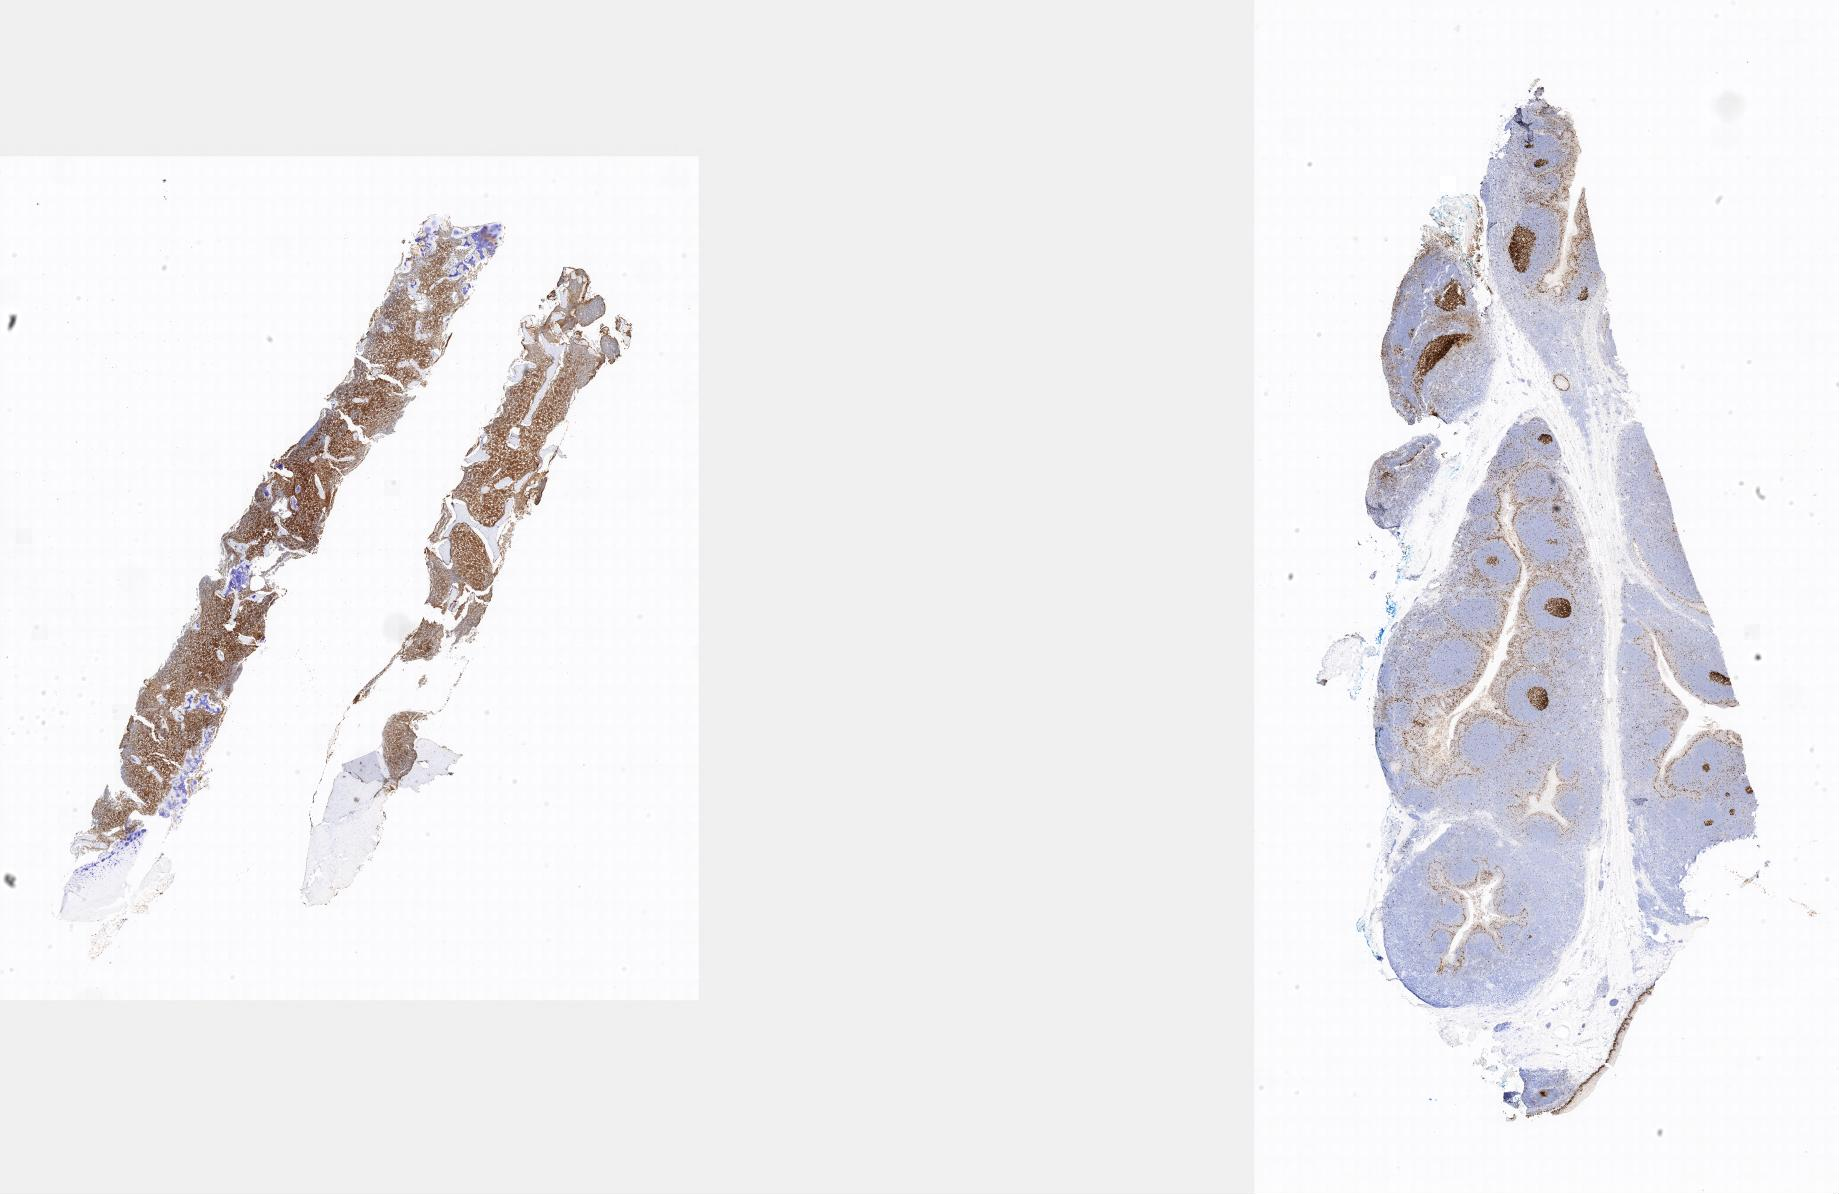
Immunohistochemistry (IHC) whole-slide image stained for Ki-67 — a low-resolution overview of the entire scanned area. Tumor tissue. Anatomic site: bone marrow. Male patient, 16 years old.
Diagnosis: Burkitt lymphoma, NOS.